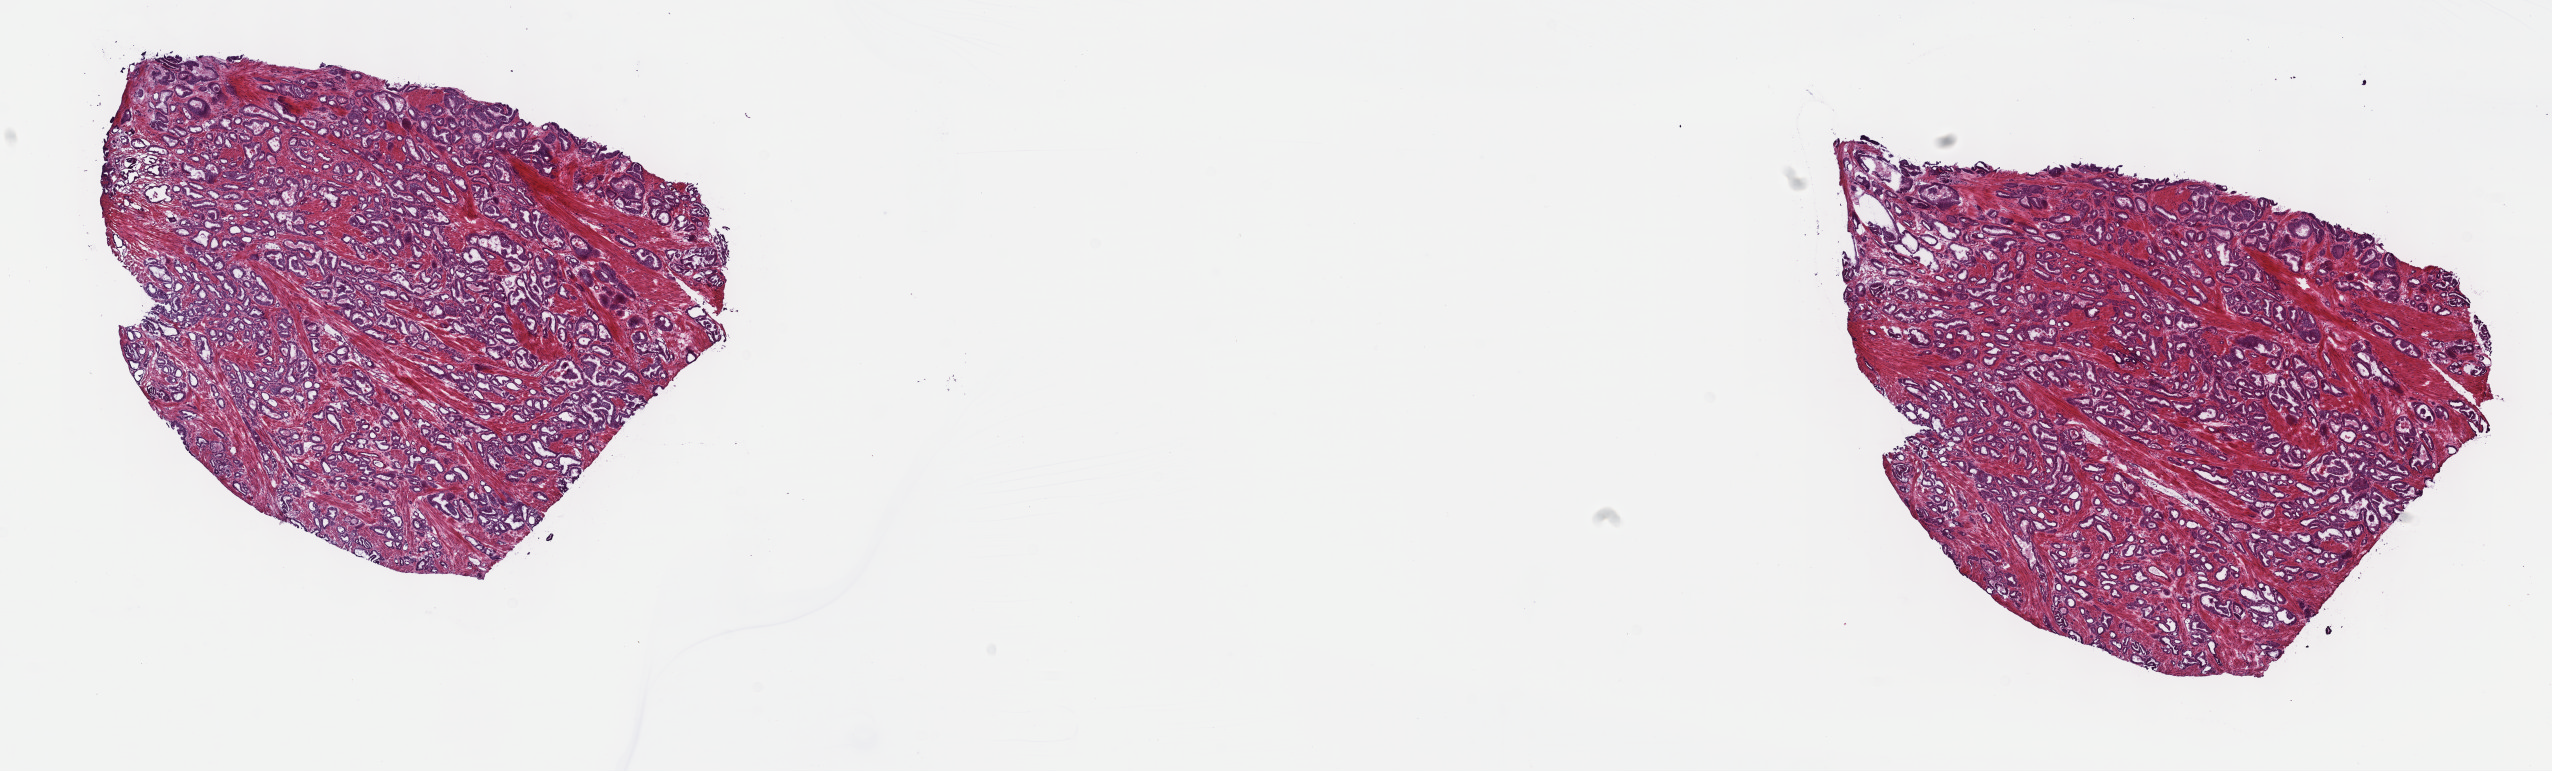
H&E-stained whole-slide image — whole scanned area (about 20.6 x 6.2 mm, acquisition: 40x scan) shown as a low-resolution overview; frozen section; primary tumour sample from the prostate. Male patient; age at initial diagnosis 57 years. Gleason score: 7 (3+4). Composition of this section per pathologist review: tumour cells 100%, tumour nuclei 70%, normal cells 0%, stromal cells 0%, necrosis 0%. Inflammatory infiltration, as recorded: lymphocyte infiltration 0%, monocyte infiltration 0%, neutrophil infiltration 0%.
Laterality: right. Diagnosis: Adenocarcinoma, NOS.